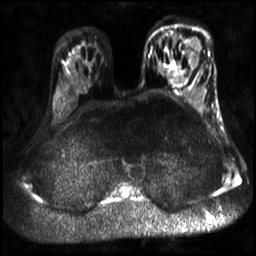
Breast MRI, one axial slice. Position 19 of 30 along the scan axis. Diffusion-weighted series; image 2 of 4 stored at this slice position (different b-values; order by instance number). 3 T. 4 mm slice thickness. 256 × 256 image matrix, field of view 320 × 320 mm. Female patient.
Outlined on this slice (expert manual segmentation):
- tumour on diffusion-weighted imaging: bounding box <186,42,202,66> (left, top, right, bottom; pixels)